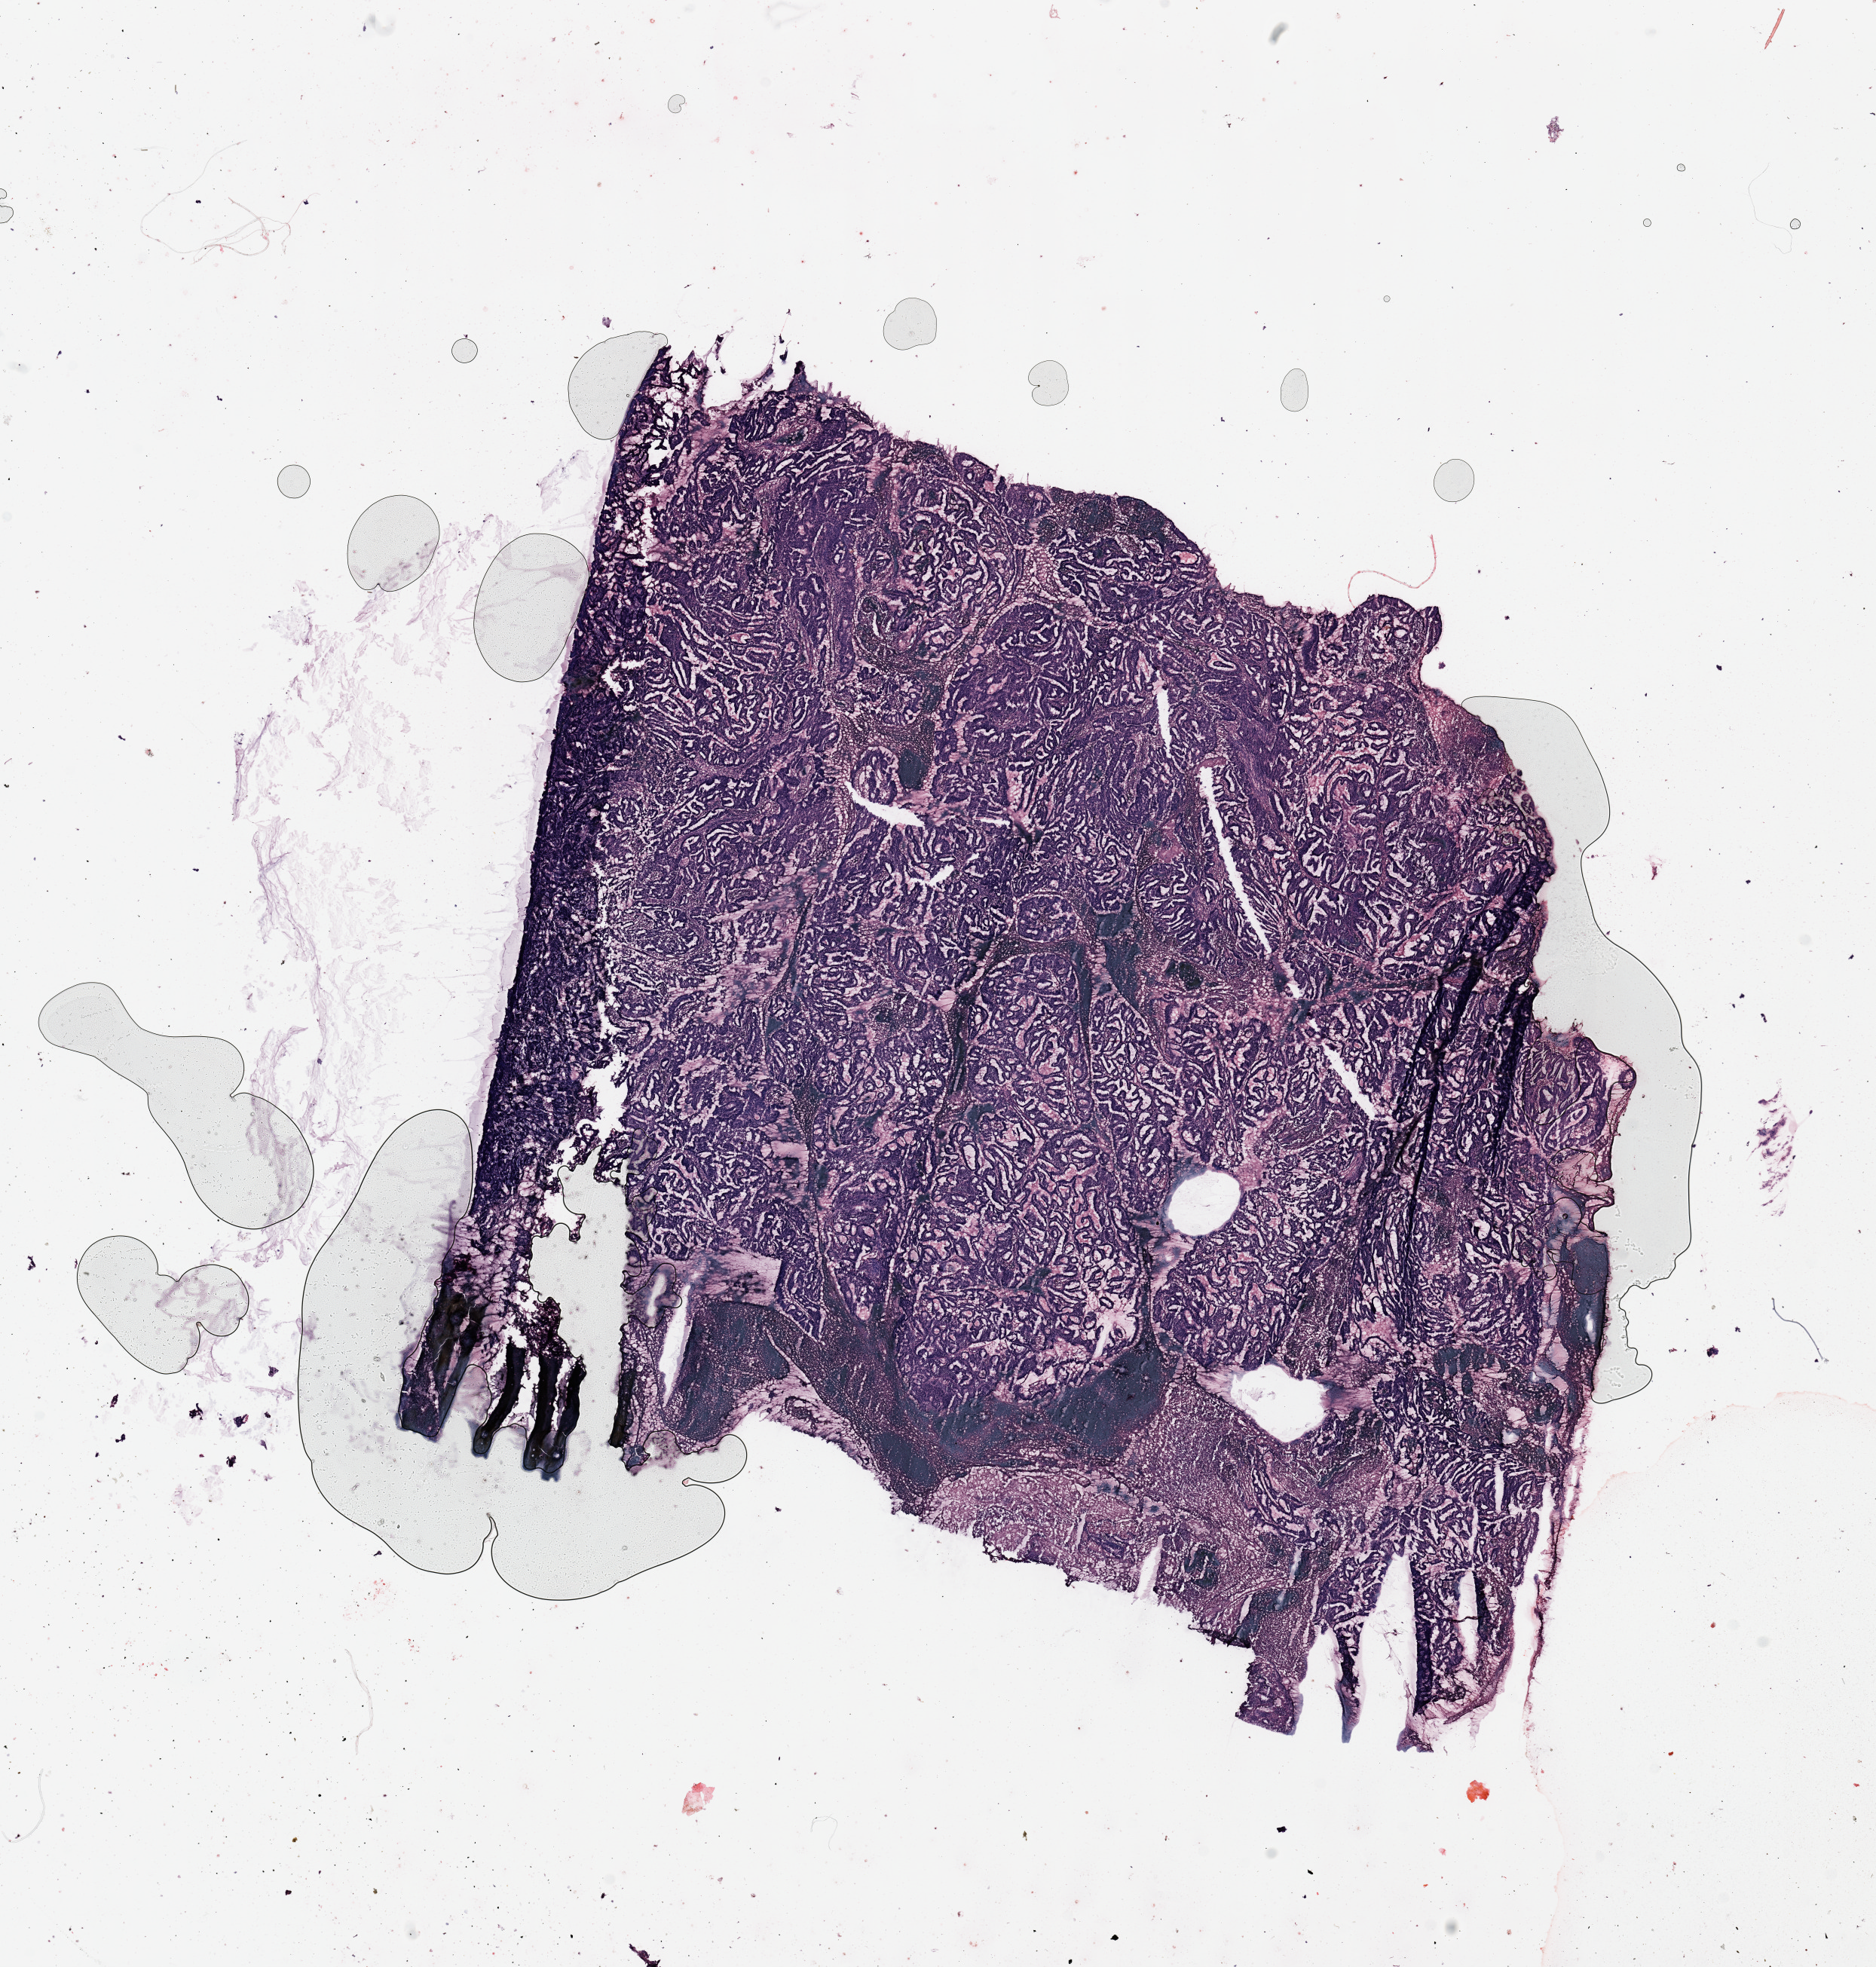
Whole-slide histology image, H&E, low-resolution overview of the scanned area, about 19.7 x 20.6 mm (from a 20x scan), tumour tissue sample, sampled site: uterus. Patient: female, age 64 years.
Histologic diagnosis: Endometrioid adenocarcinoma, NOS.